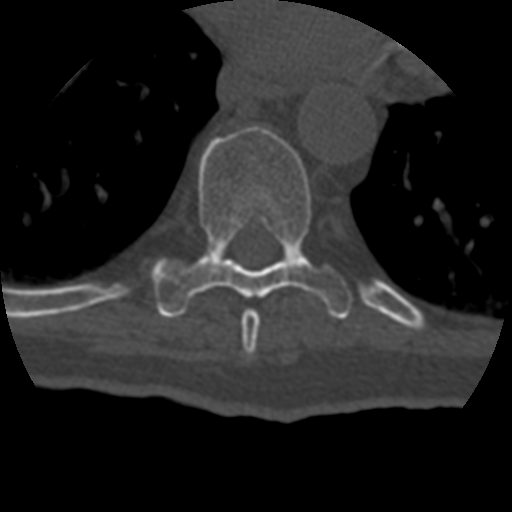
CT including the spine, one axial slice. Slice 241 of 399 in the series (ordered by position). Reconstruction kernel STANDARD. 120 kVp. Bone window (W 1800 / L 400 HU). 512 × 512 image matrix. Patient age 69 years. From the clinical record (not read from this slice): primary cancer: prostate.
Annotated regions visible in this slice (semi-automatically segmented with operator editing):
- T8 vertebra: box from (x=242, y=309) to (x=260, y=355) px
- T9 vertebra: (x=151, y=126)–(x=352, y=319)